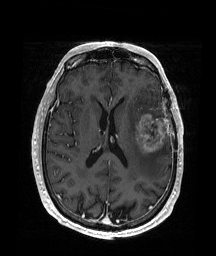
Brain MRI from a brain-tumour surgery series, one axial slice; position 83 of 176 along the scan axis; T1-weighted post-contrast; 216 × 256 image matrix. From the clinical record (not read from this slice): histopathology: Glioblastoma; WHO grade: 4; IDH mutation: no; tumour location: Left Frontal.
Structures marked on this image (expert manual segmentation):
- tumour: bounding box (x1, y1, x2, y2) in pixels: (135, 113, 169, 153)